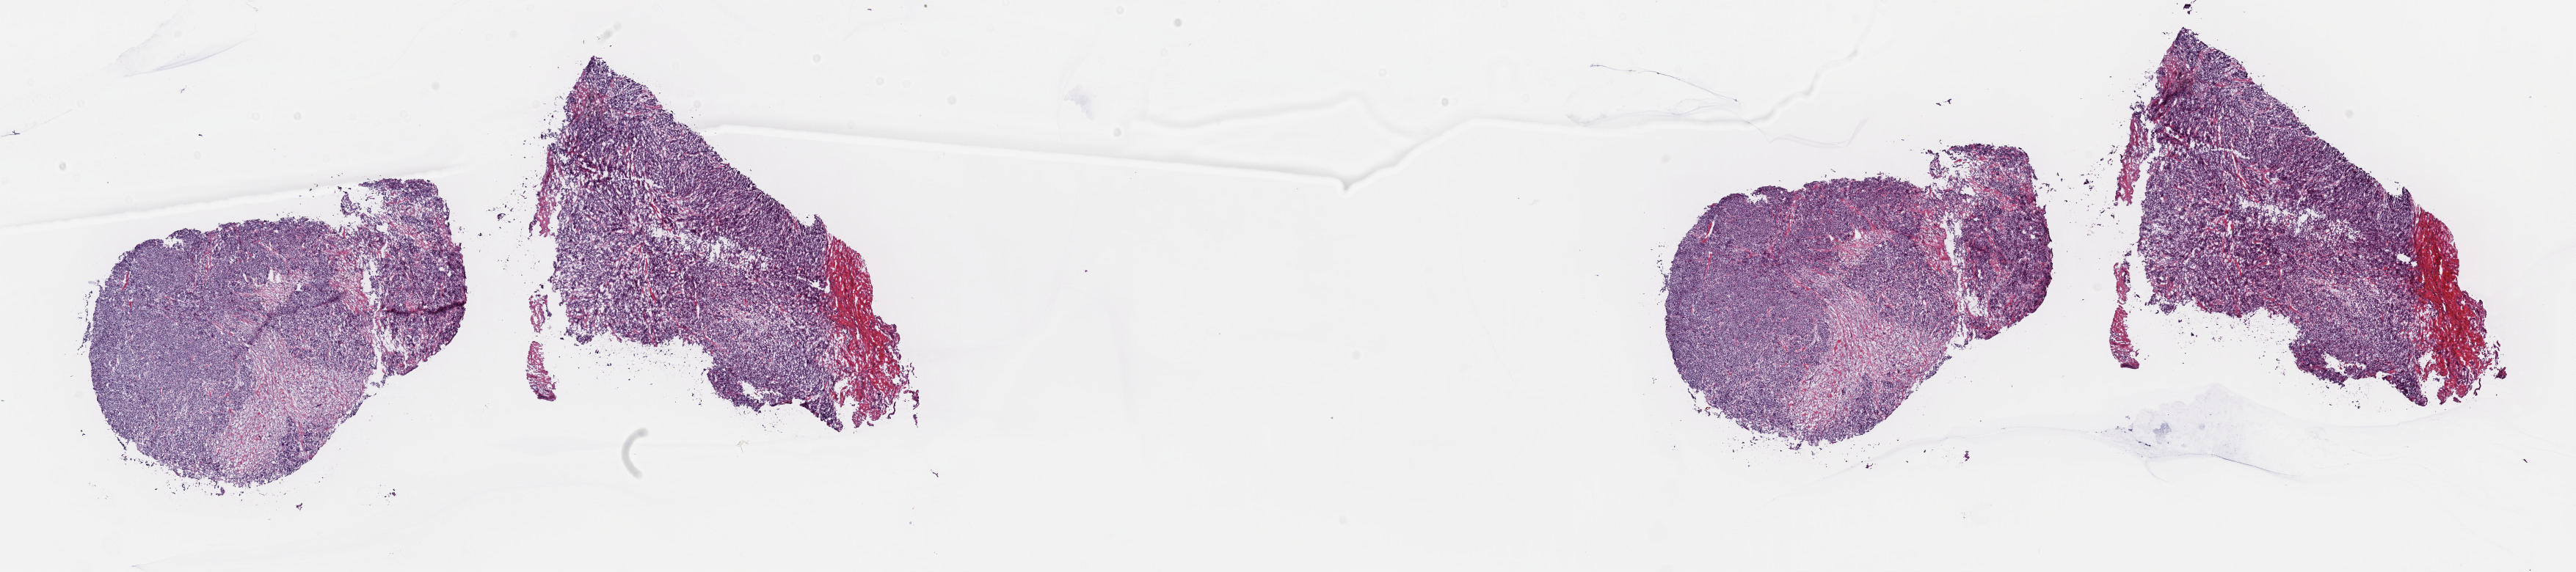
H&E whole-slide image — low-resolution overview of the scanned area, about 27.7 x 6.2 mm; frozen section from the top of the tissue portion; metastatic tumour sample, sampled site: abdomen. Female patient; age at initial diagnosis 55 years. Slide review estimates, as recorded: tumour cells 90%, tumour nuclei 90%, normal cells 0%, stromal cells 10%, necrosis 0%. Inflammatory infiltration, as recorded: lymphocyte infiltration 0%, monocyte infiltration 0%, neutrophil infiltration 0%.
This section: metastatic tumour tissue. Patient diagnosis: Malignant melanoma, NOS.